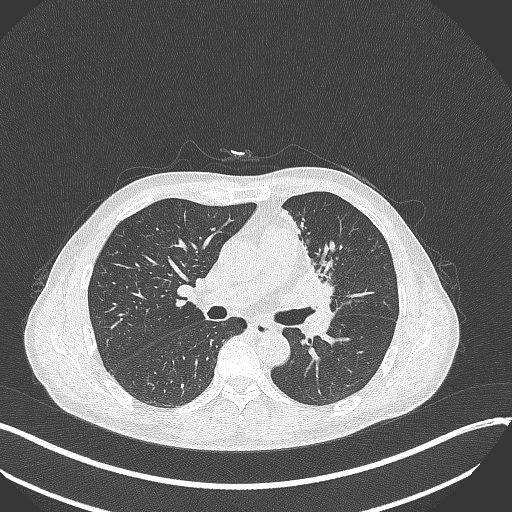
Chest CT, one axial slice. Position 190 of 411 along the scan axis. Reconstruction kernel B70f. Lung window (W 1500 / L -600 HU). 512 × 512 image matrix. Patient: male, 56 years. Case-level facts recorded for this patient, not image findings: clinical TNM (as recorded): T2a N0 M0.
Outlined on this slice (bounding box drawn by a radiologist):
- lung tumour (recorded histology: squamous cell carcinoma): bounding box <277,268,341,314> (left, top, right, bottom; pixels)